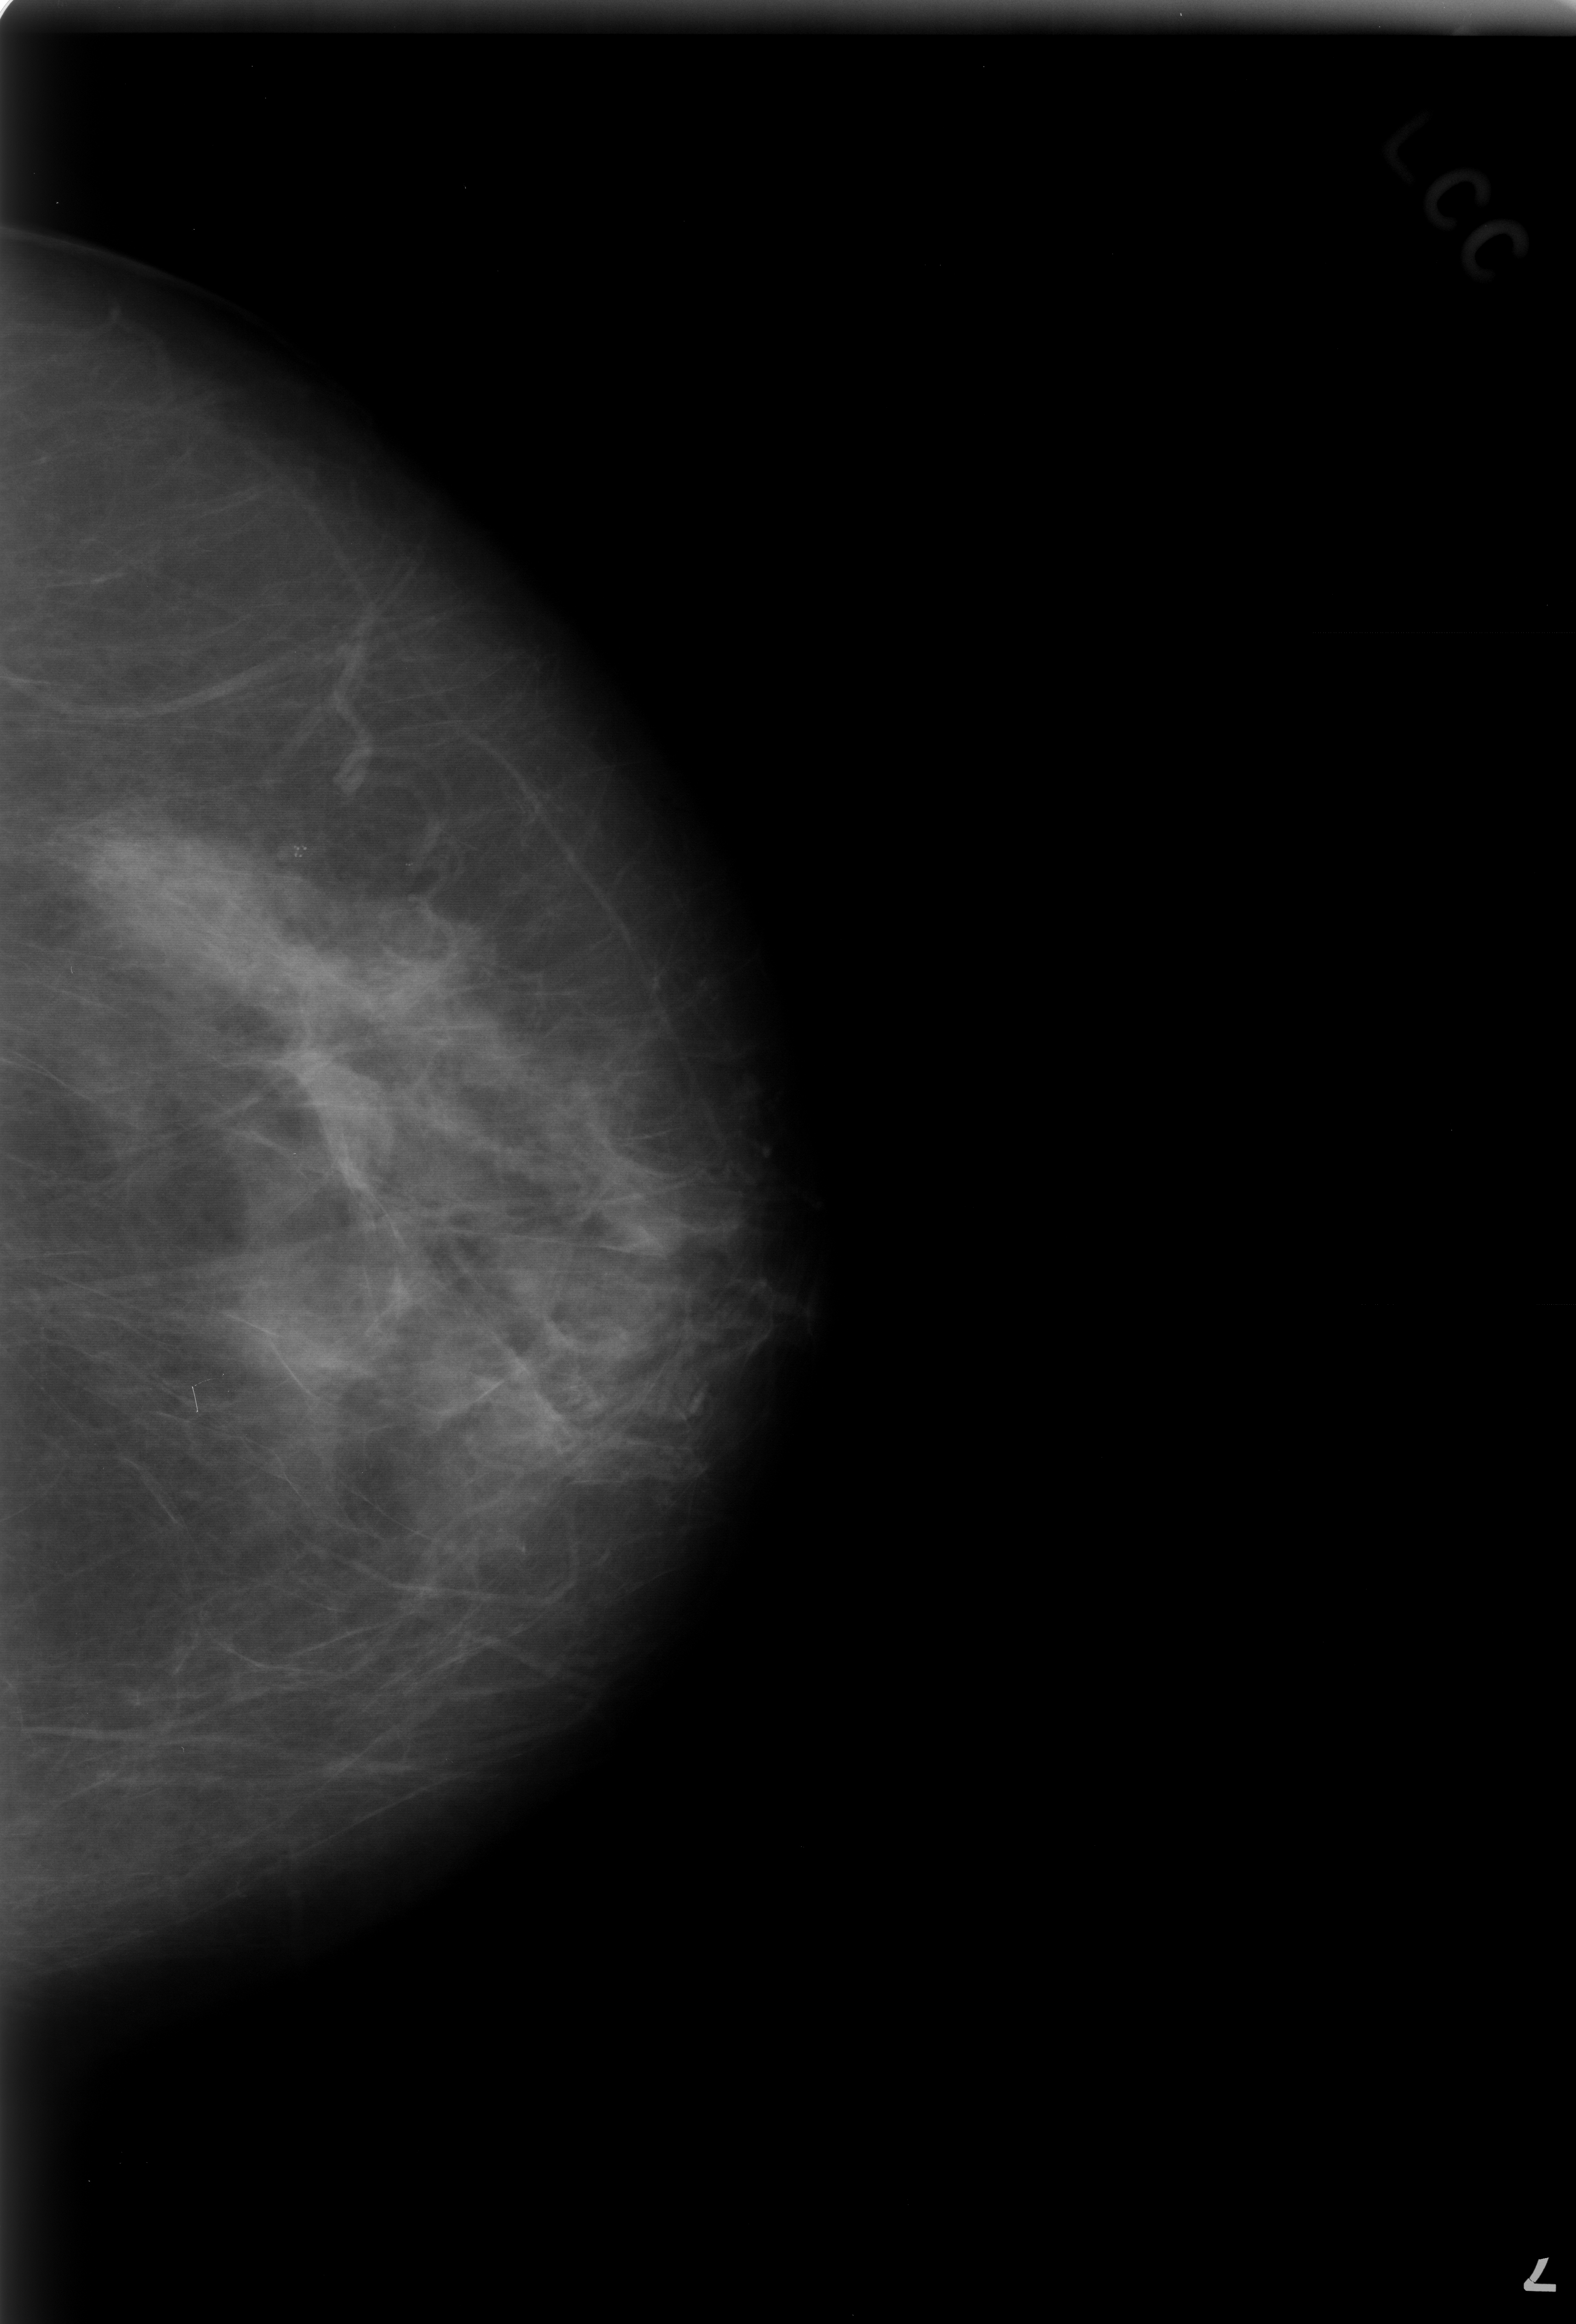
Digitized screen-film mammogram. Left breast. Craniocaudal (CC) view. Breast composition: scattered fibroglandular densities (BI-RADS density category 2 of 4). 1576 × 2324 image matrix.
Expert-marked regions of interest on this film, with their recorded descriptors:
- calcifications, morphology punctate, distribution clustered; BI-RADS assessment category 3; subtlety rating 4 on a 1 (subtle) to 5 (obvious) scale; pathology result (as recorded, not read from the image): benign: box from (x=239, y=792) to (x=388, y=915) px